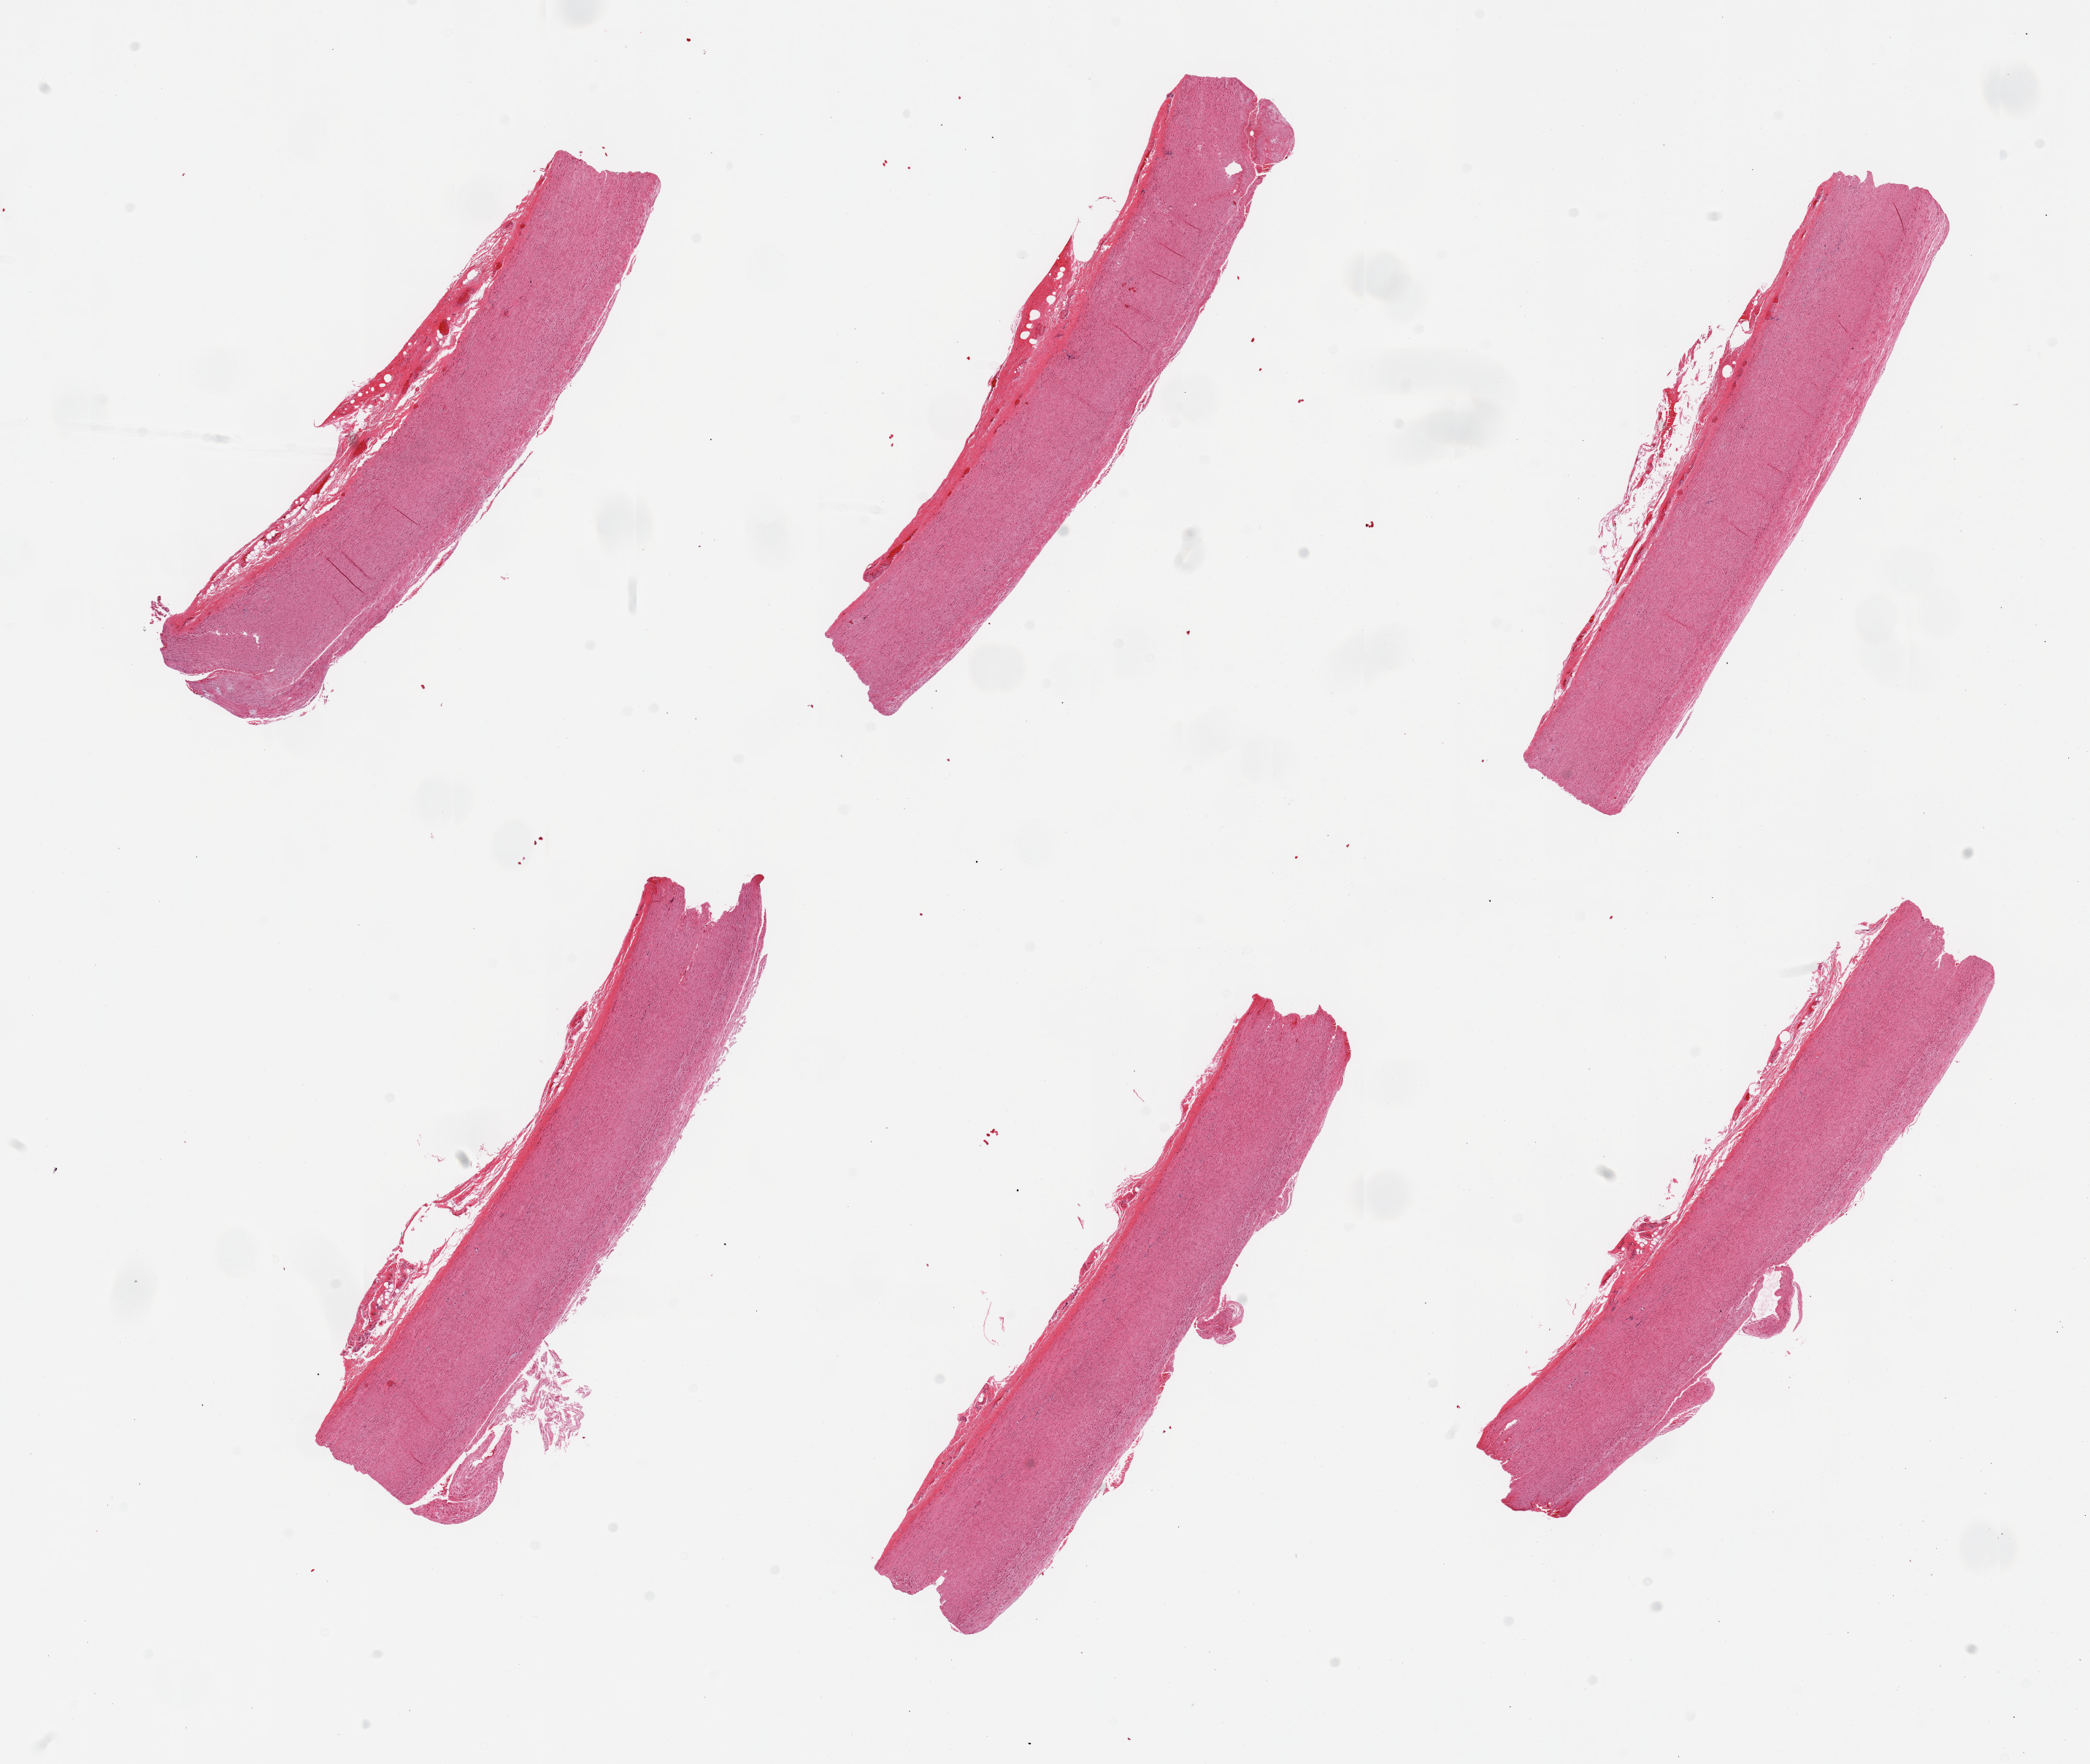
Haematoxylin and eosin whole-slide image — whole scanned area (about 22.6 x 19.1 mm) shown as a low-resolution overview; PAXgene-fixed paraffin-embedded (PFPE) section; section of aorta (target tissue); tissue donor sample. Donor: male.
* review note (as recorded): 6 pieces